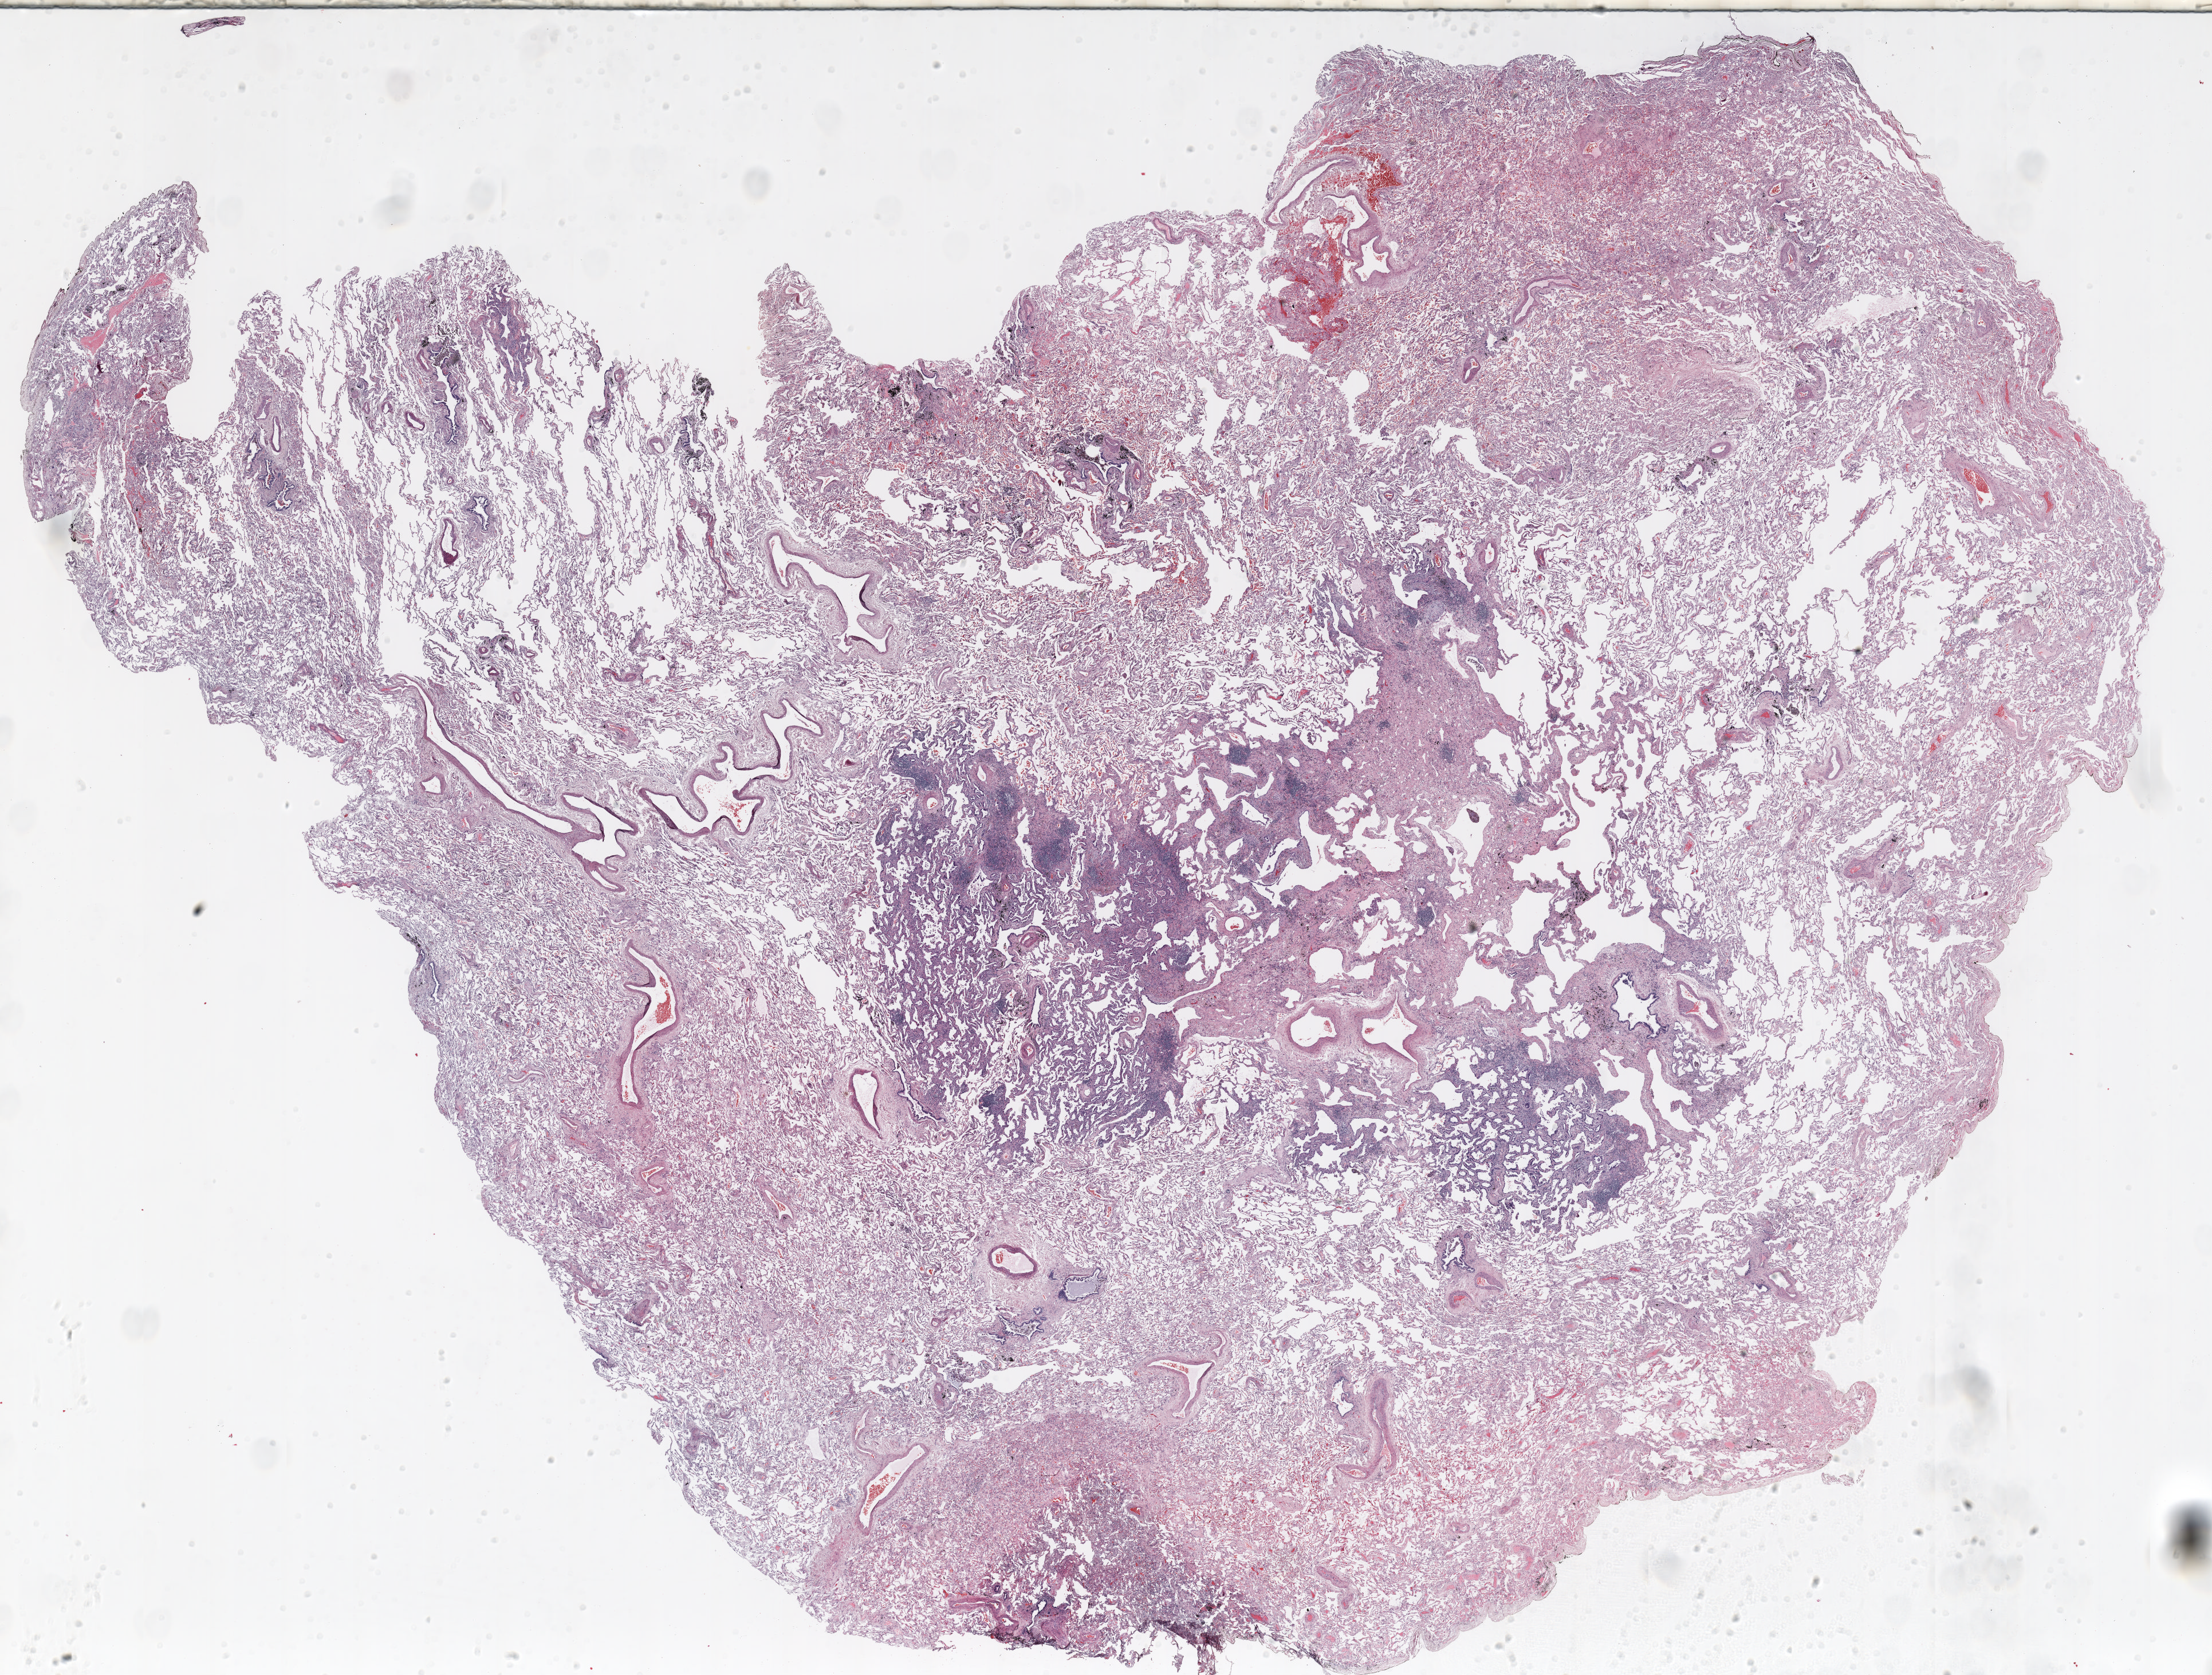
Hematoxylin and eosin (H&E) stained whole-slide image — whole scanned area (about 31.0 x 23.5 mm) shown as a low-resolution overview; formalin-fixed paraffin-embedded (FFPE) section; lung tissue. Female, age 61 at enrolment. Former smoker at enrolment.
• participant's lung-cancer diagnosis: Adenocarcinoma, NOS
• stage (AJCC 6th edition): IIIB
• primary tumour location (clinical record): left upper lobe
• tumour size (pathology): 15 mm
• ICD-O-3 topography: upper lobe of lung (C34.1)